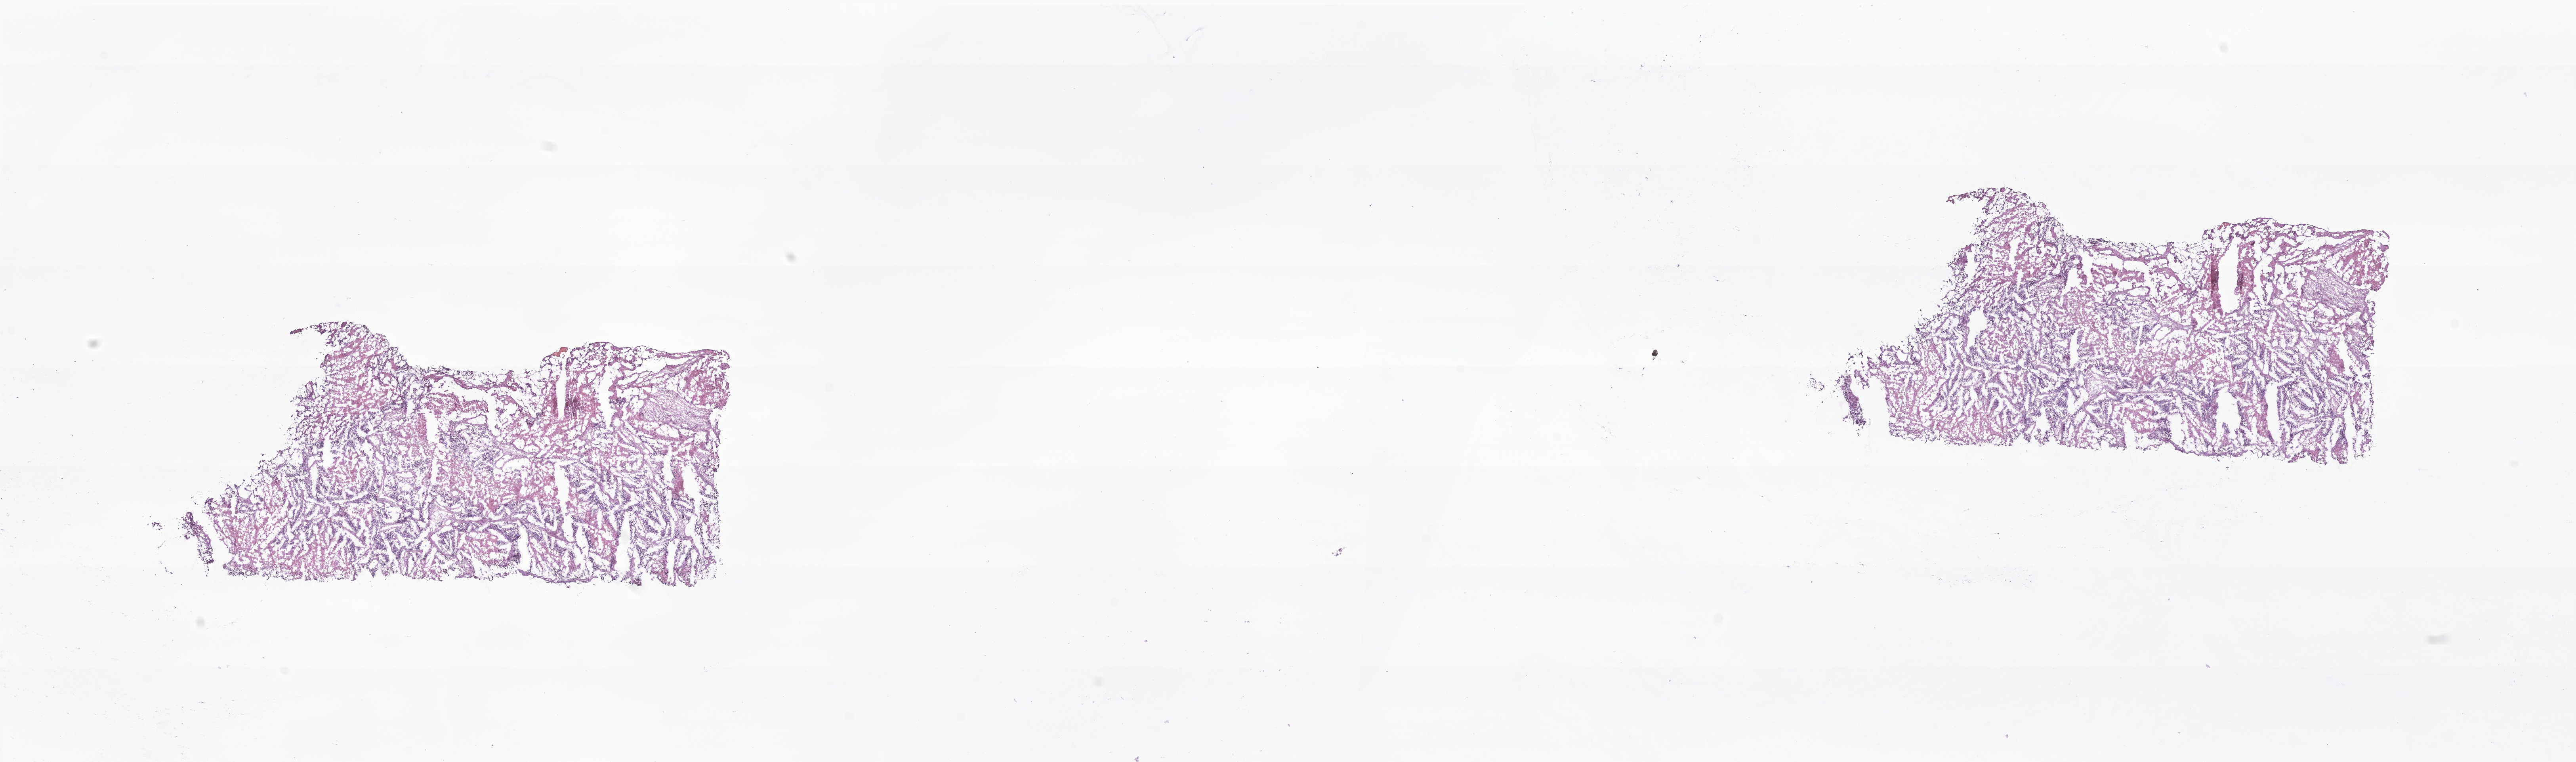
H&E whole-slide image of tumor tissue from the adrenal gland, a low-resolution overview of the entire scanned area, about 27.4 x 8.1 mm. Frozen section (OCT-embedded). Male patient, age 42 months (3 years 6 months).
* diagnosis: Neuroblastoma, NOS